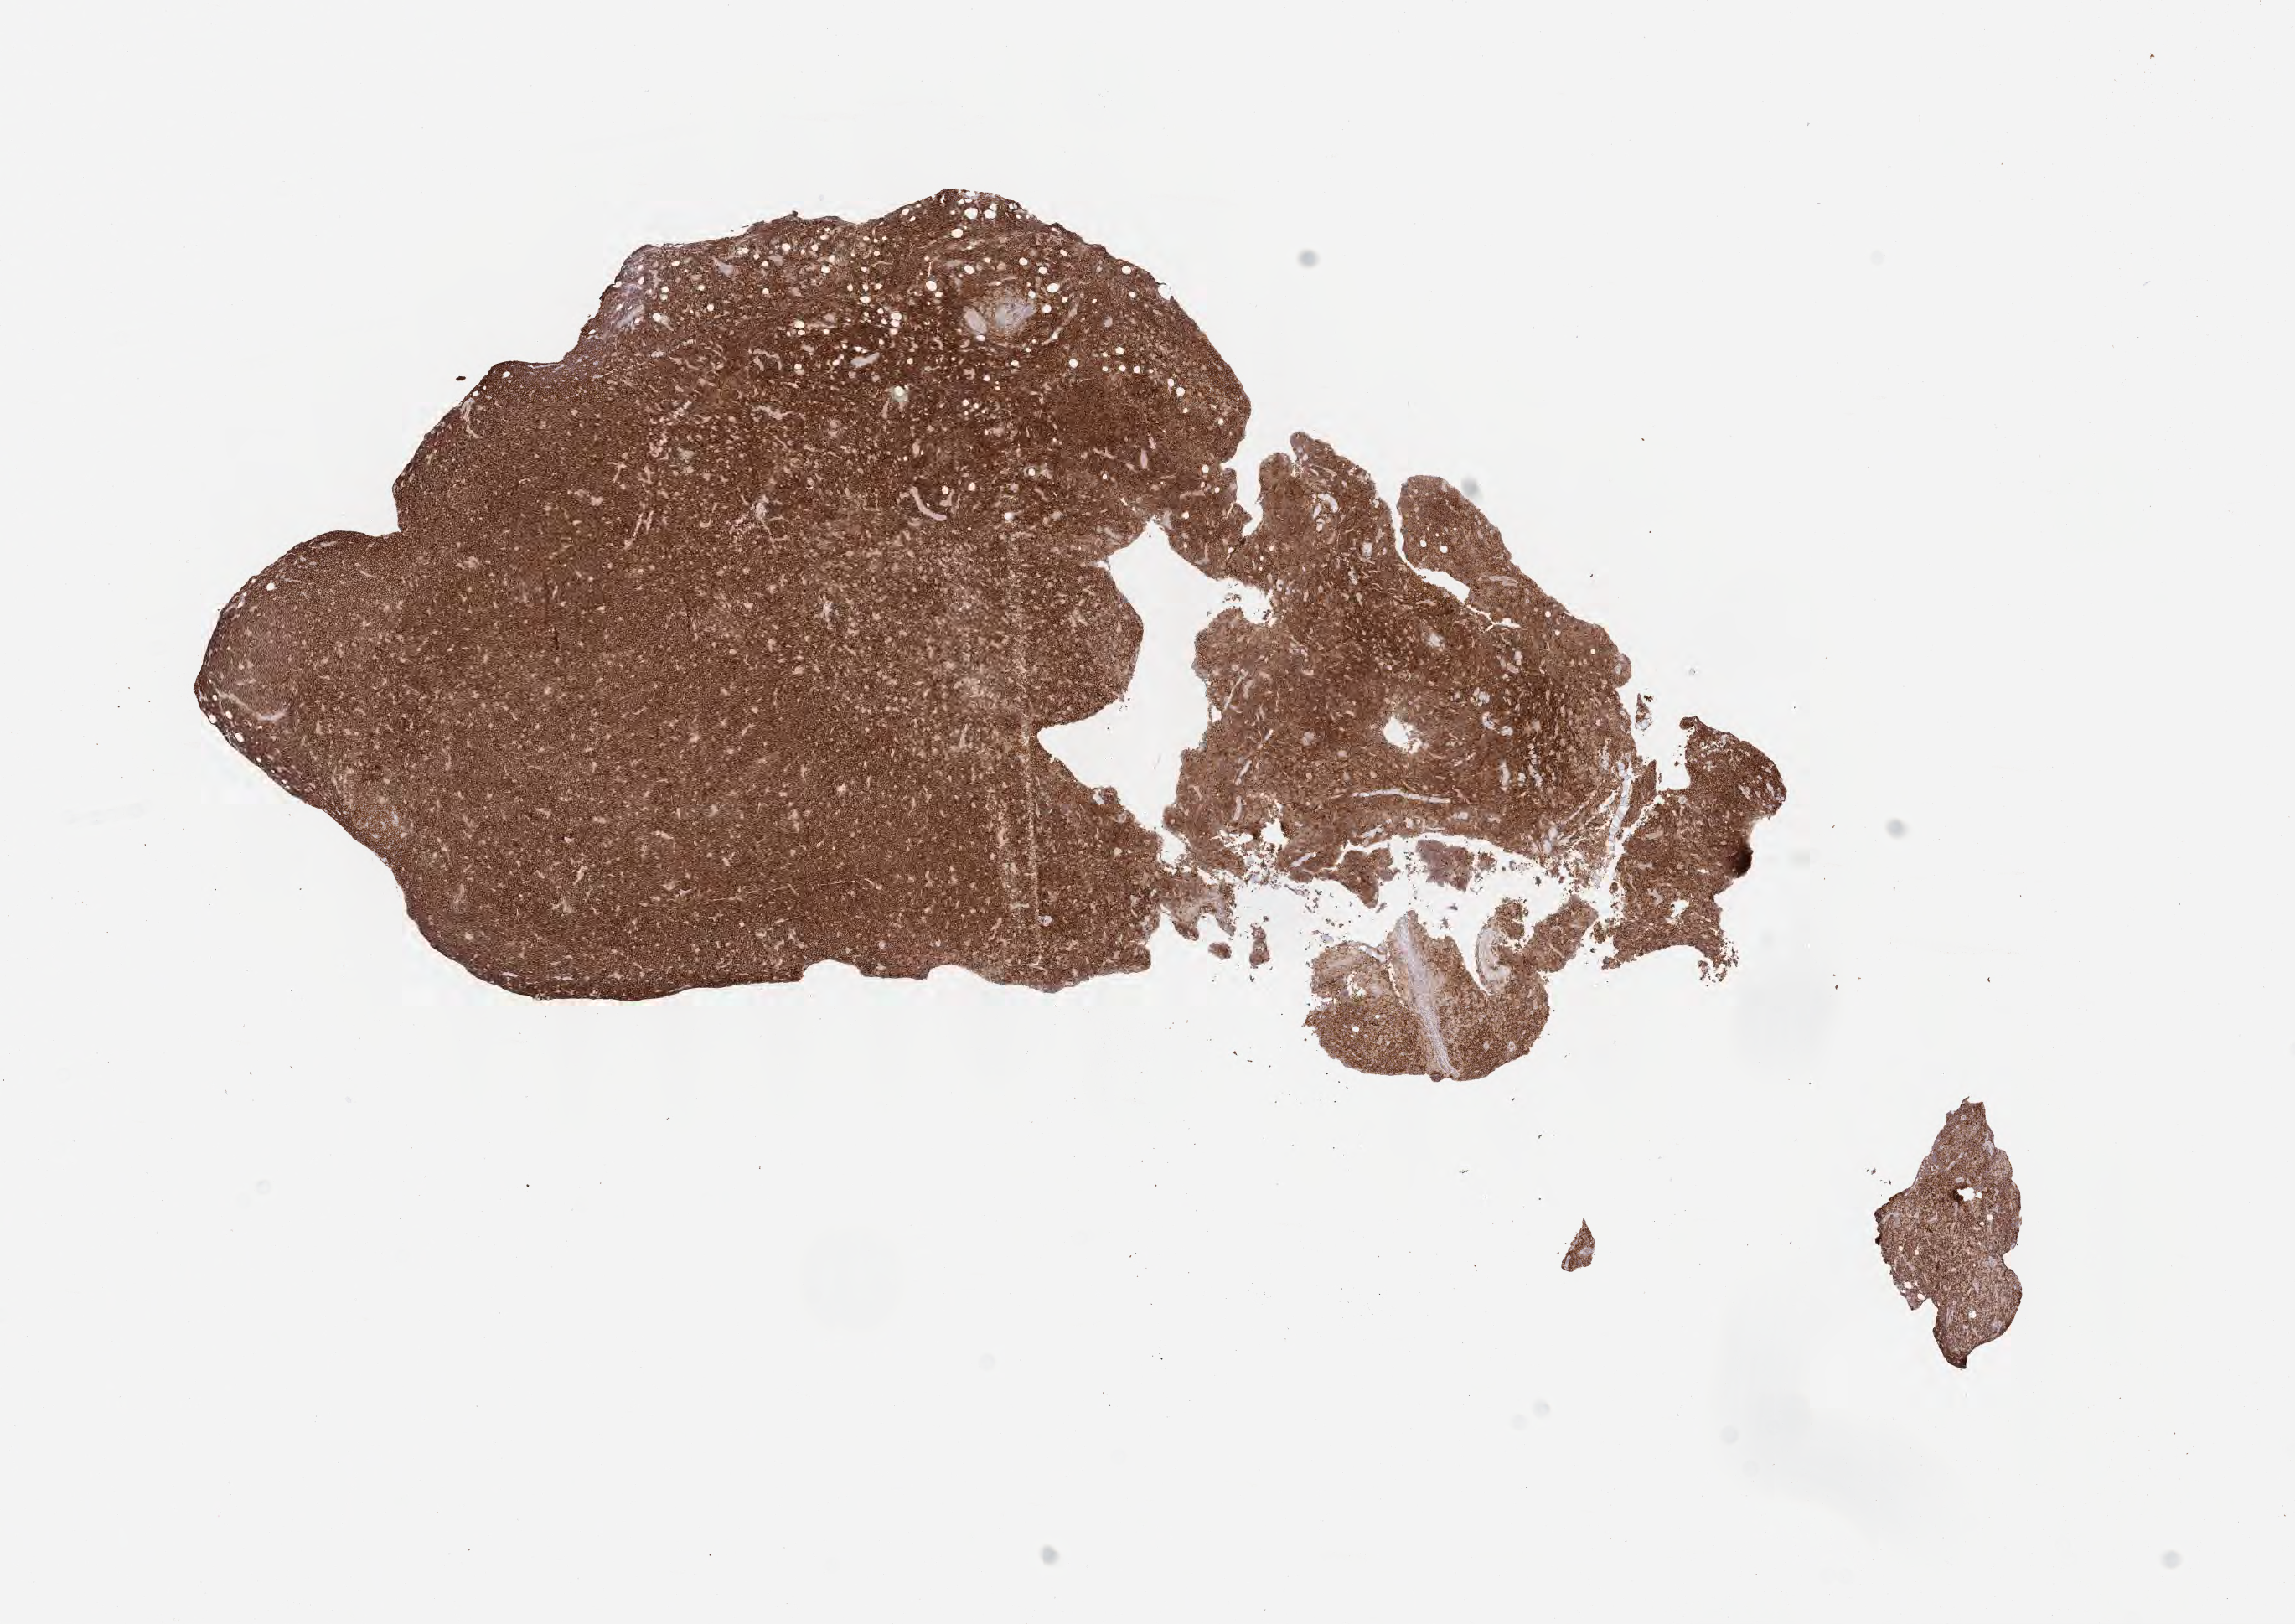
IHC for CD10, whole-slide image — whole scanned area (about 11.1 x 7.8 mm) shown as a low-resolution overview. Specimen: tumor tissue. Patient female; aged 40.
* diagnosis: Burkitt lymphoma, NOS